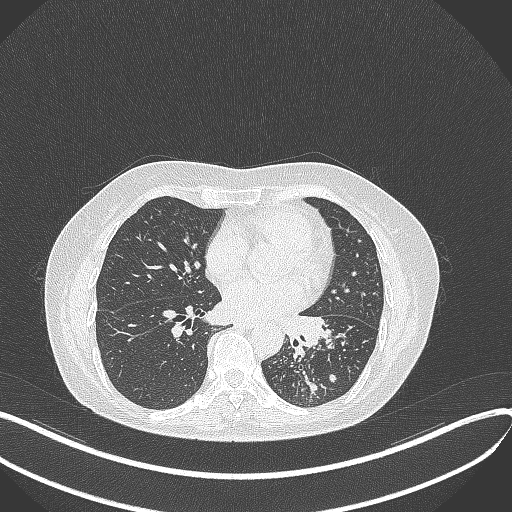
Chest CT, one axial slice; position 182 of 429 along the scan axis; reconstruction kernel B70f; 100 kVp; lung window (W 1500 / L -600 HU); 512 × 512 image matrix, field of view 400 × 400 mm. Patient: female, 63 years. Case-level facts recorded for this patient, not image findings: clinical TNM (as recorded): T1b N0 M0; histopathological grade: G2-3.
Annotated regions visible in this slice (rectangle marked by the reading radiologist):
- lung tumour (recorded histology: adenocarcinoma): bounding box [x1, y1, x2, y2] px = [276, 308, 328, 347]